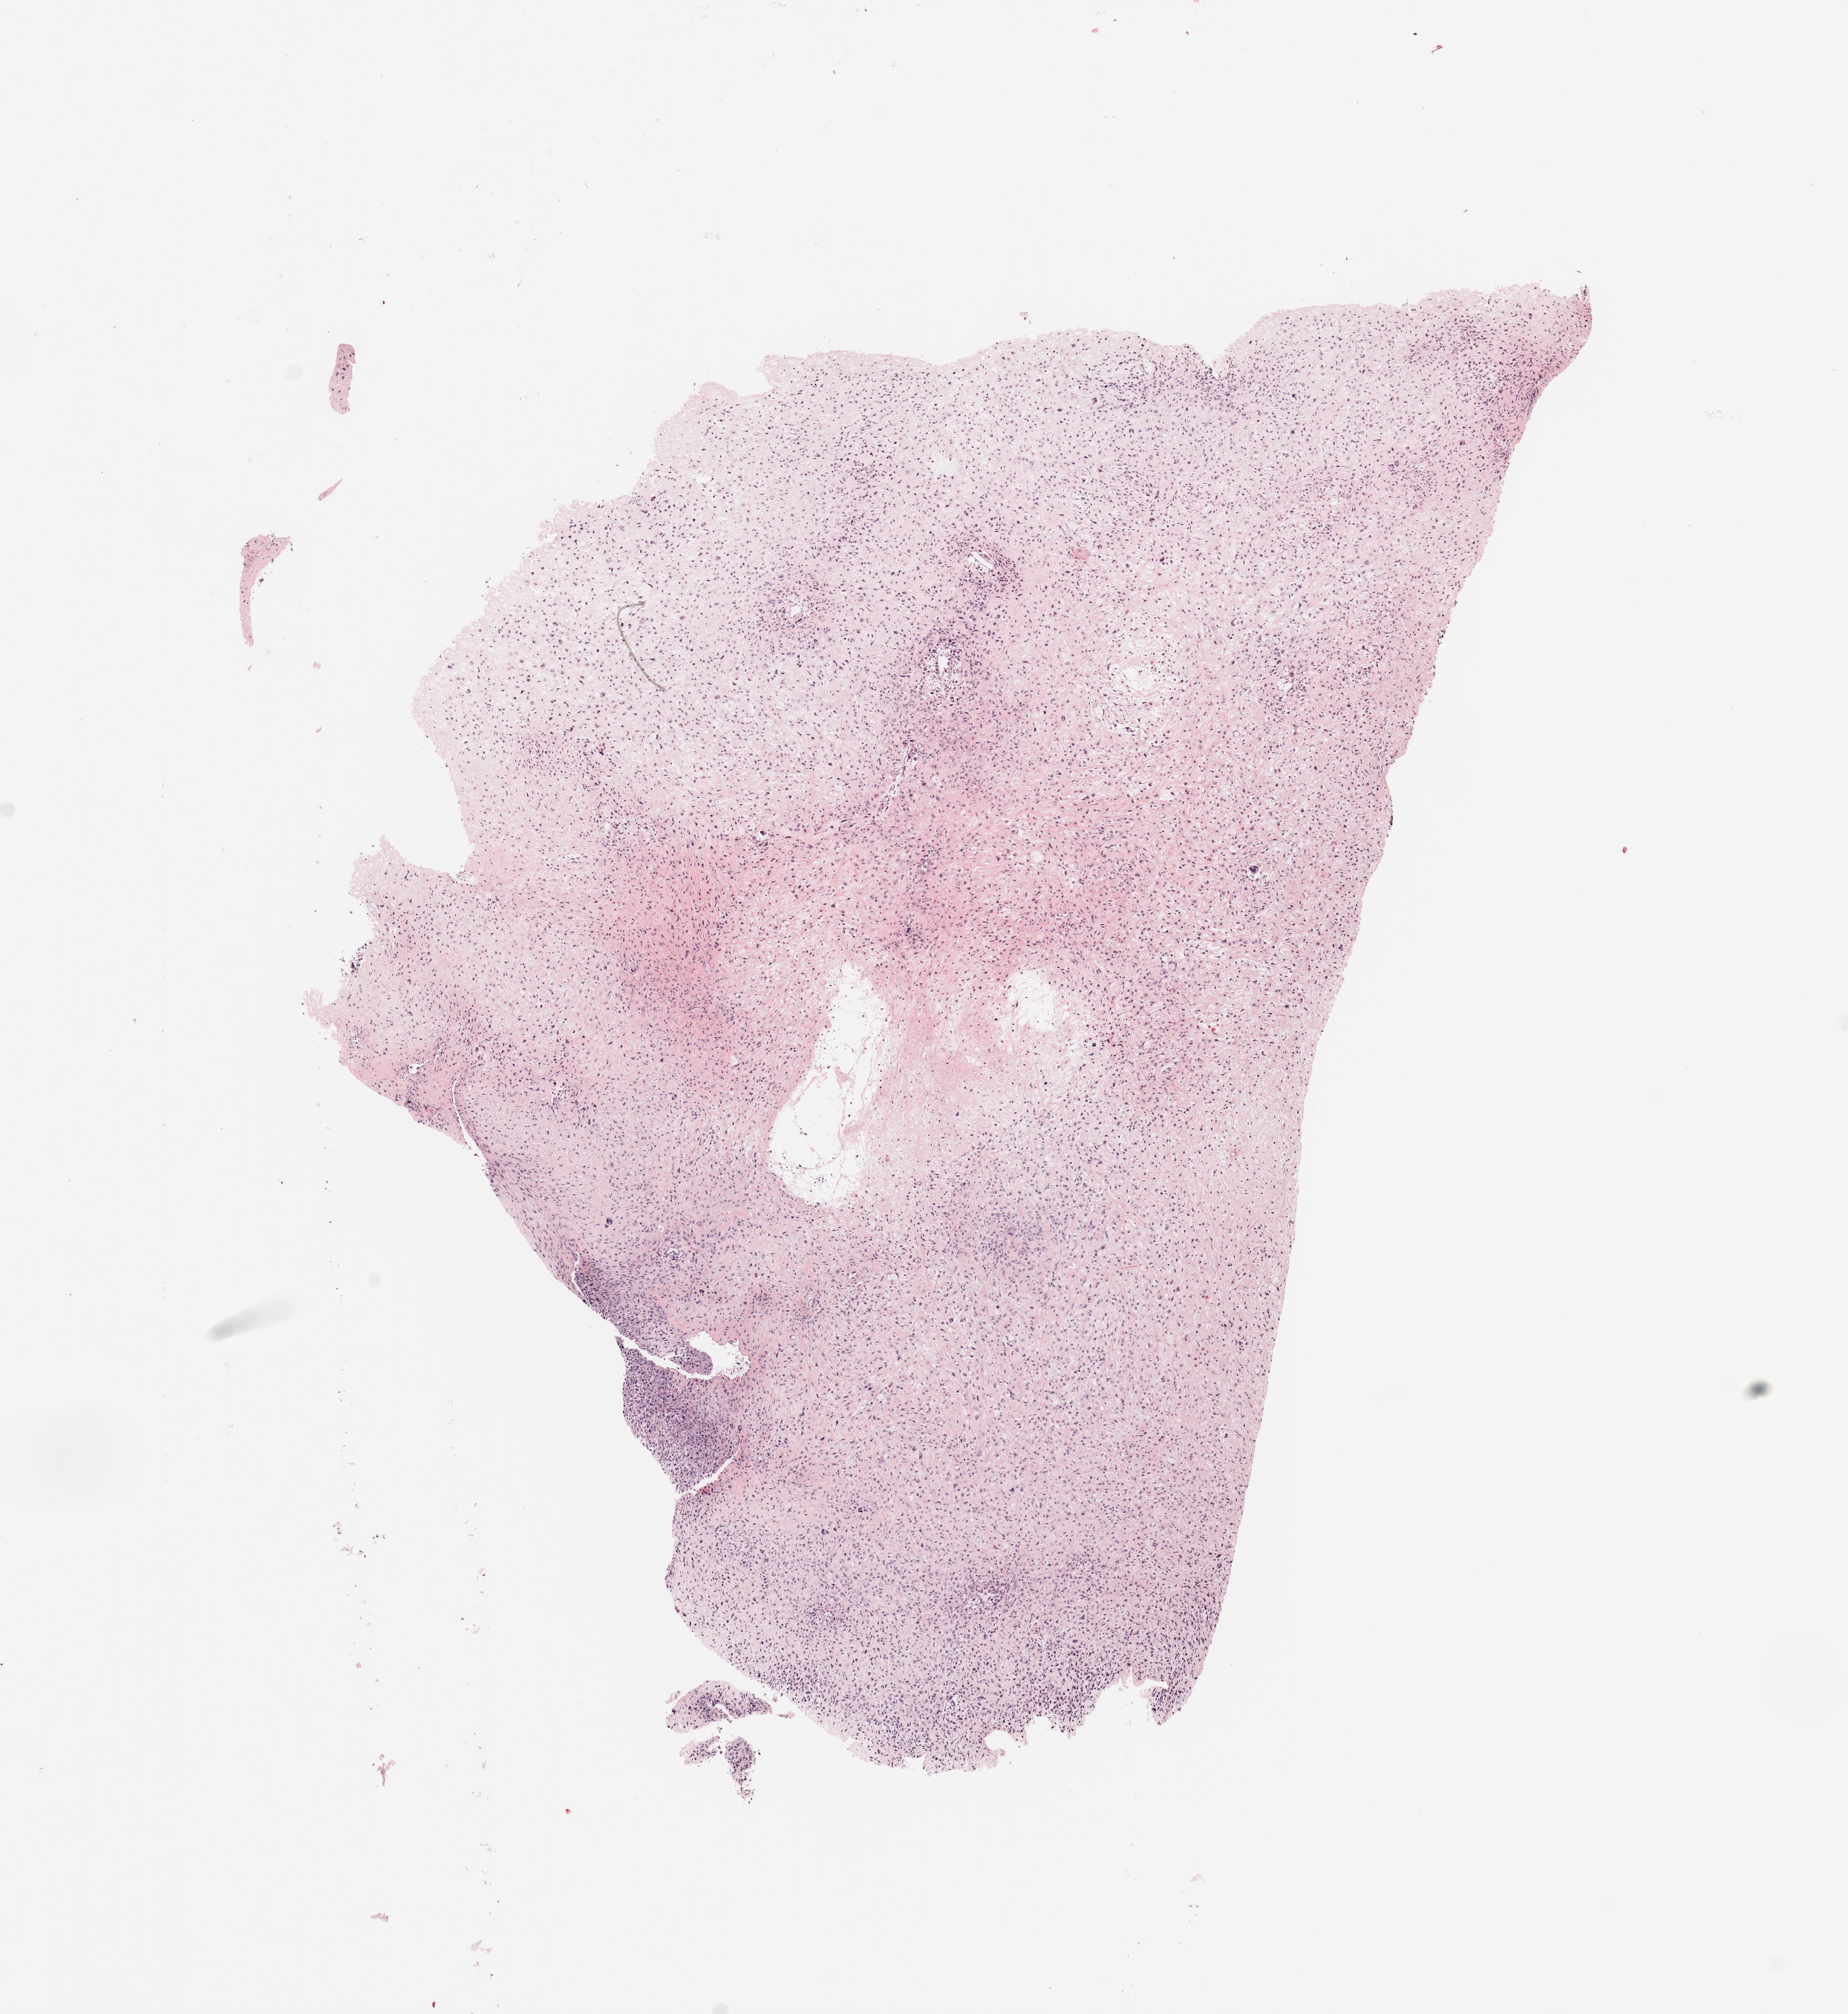
H&E whole-slide image — a low-resolution overview of the entire scanned area, about 9.8 x 10.7 mm (from a 20x scan); tumour tissue sample. Female, 80 y/o.
Primary tumour site (as recorded): lower extremity. Patient diagnosis (cohort enrolment): sarcoma (site not recorded at cohort level).